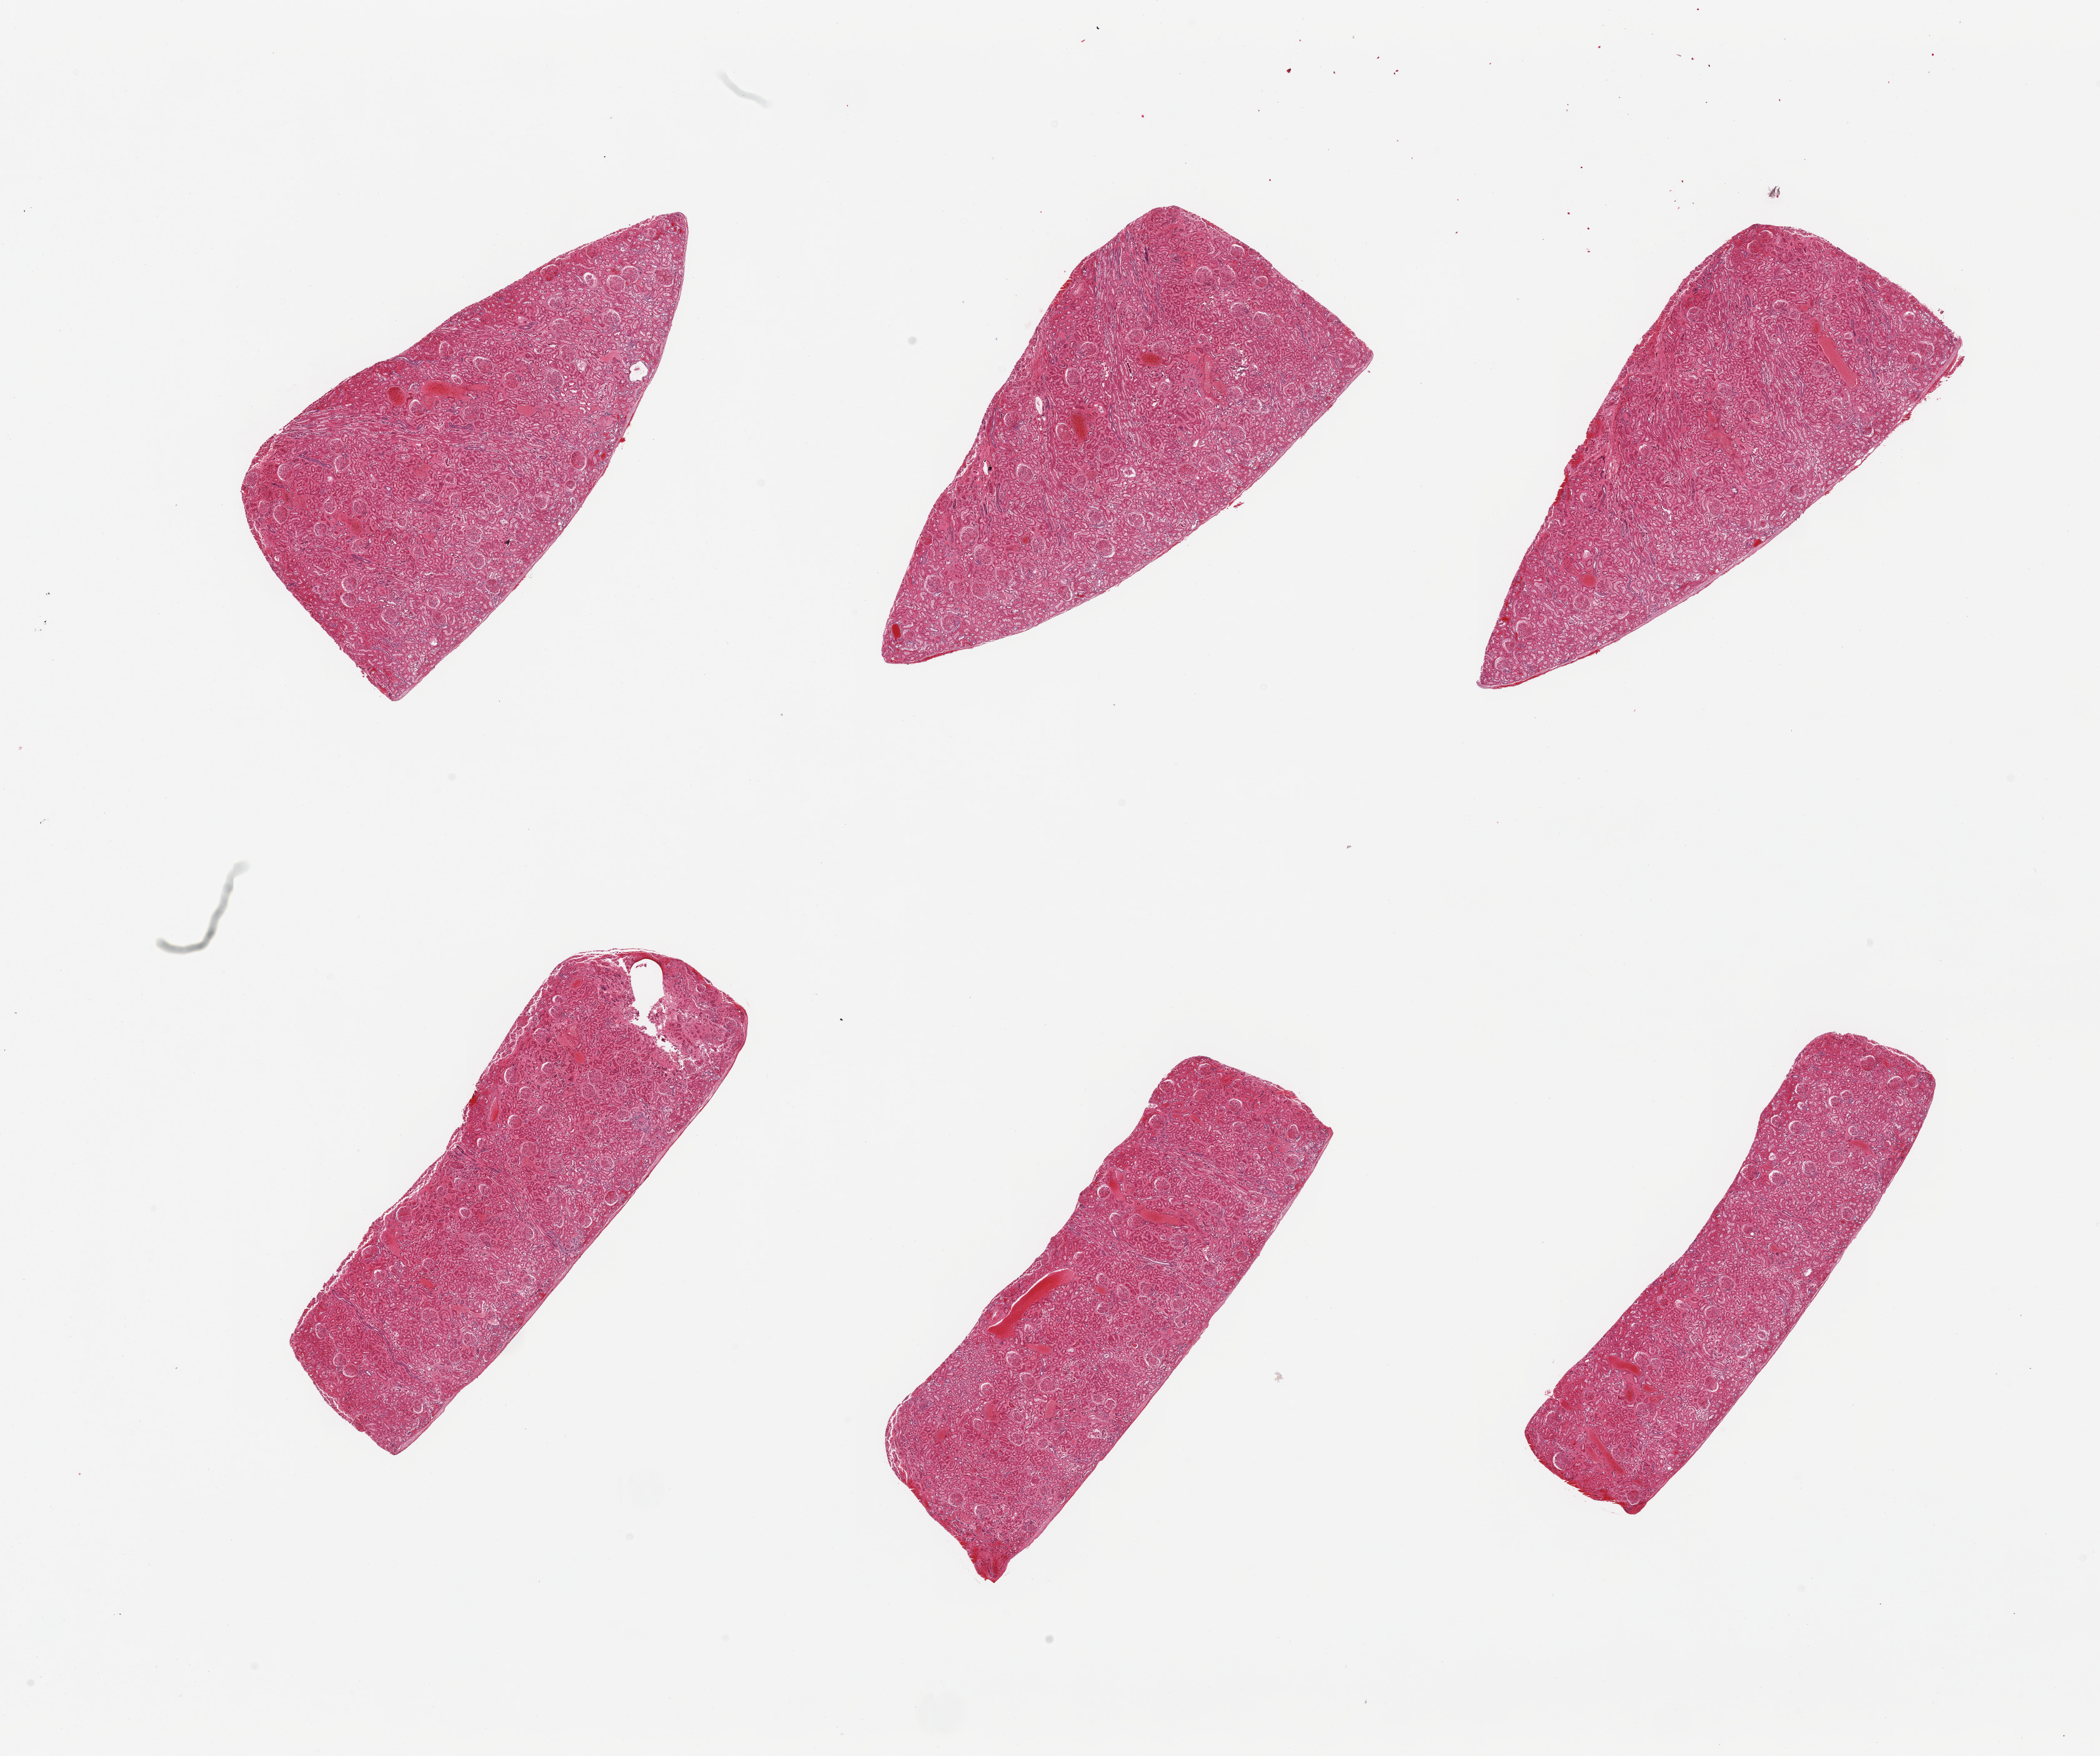
Whole-slide image, hematoxylin and eosin (H&E) stain, shown as a low-resolution overview of the whole scanned area (about 26.6 x 22.2 mm, slide scanned at 20x). PAXgene-fixed, paraffin-embedded tissue. Section of renal cortex (target tissue). Donor tissue sample. Male donor.
• review note (as recorded): 6 pieces; no active or chronic lesions